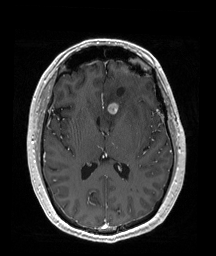
Brain MRI from a brain-tumour surgery series, one axial slice; position 92 of 192 along the scan axis; T1-weighted post-contrast; 216 × 256 image matrix. From the clinical record (not read from this slice): histopathology: Oligodendroglioma; WHO grade: 2; IDH mutation: yes; tumour location: Left Frontal (septal).
Structures marked on this image (manually delineated by an expert):
- tumour: bounding box <107,102,132,114> (left, top, right, bottom; pixels)